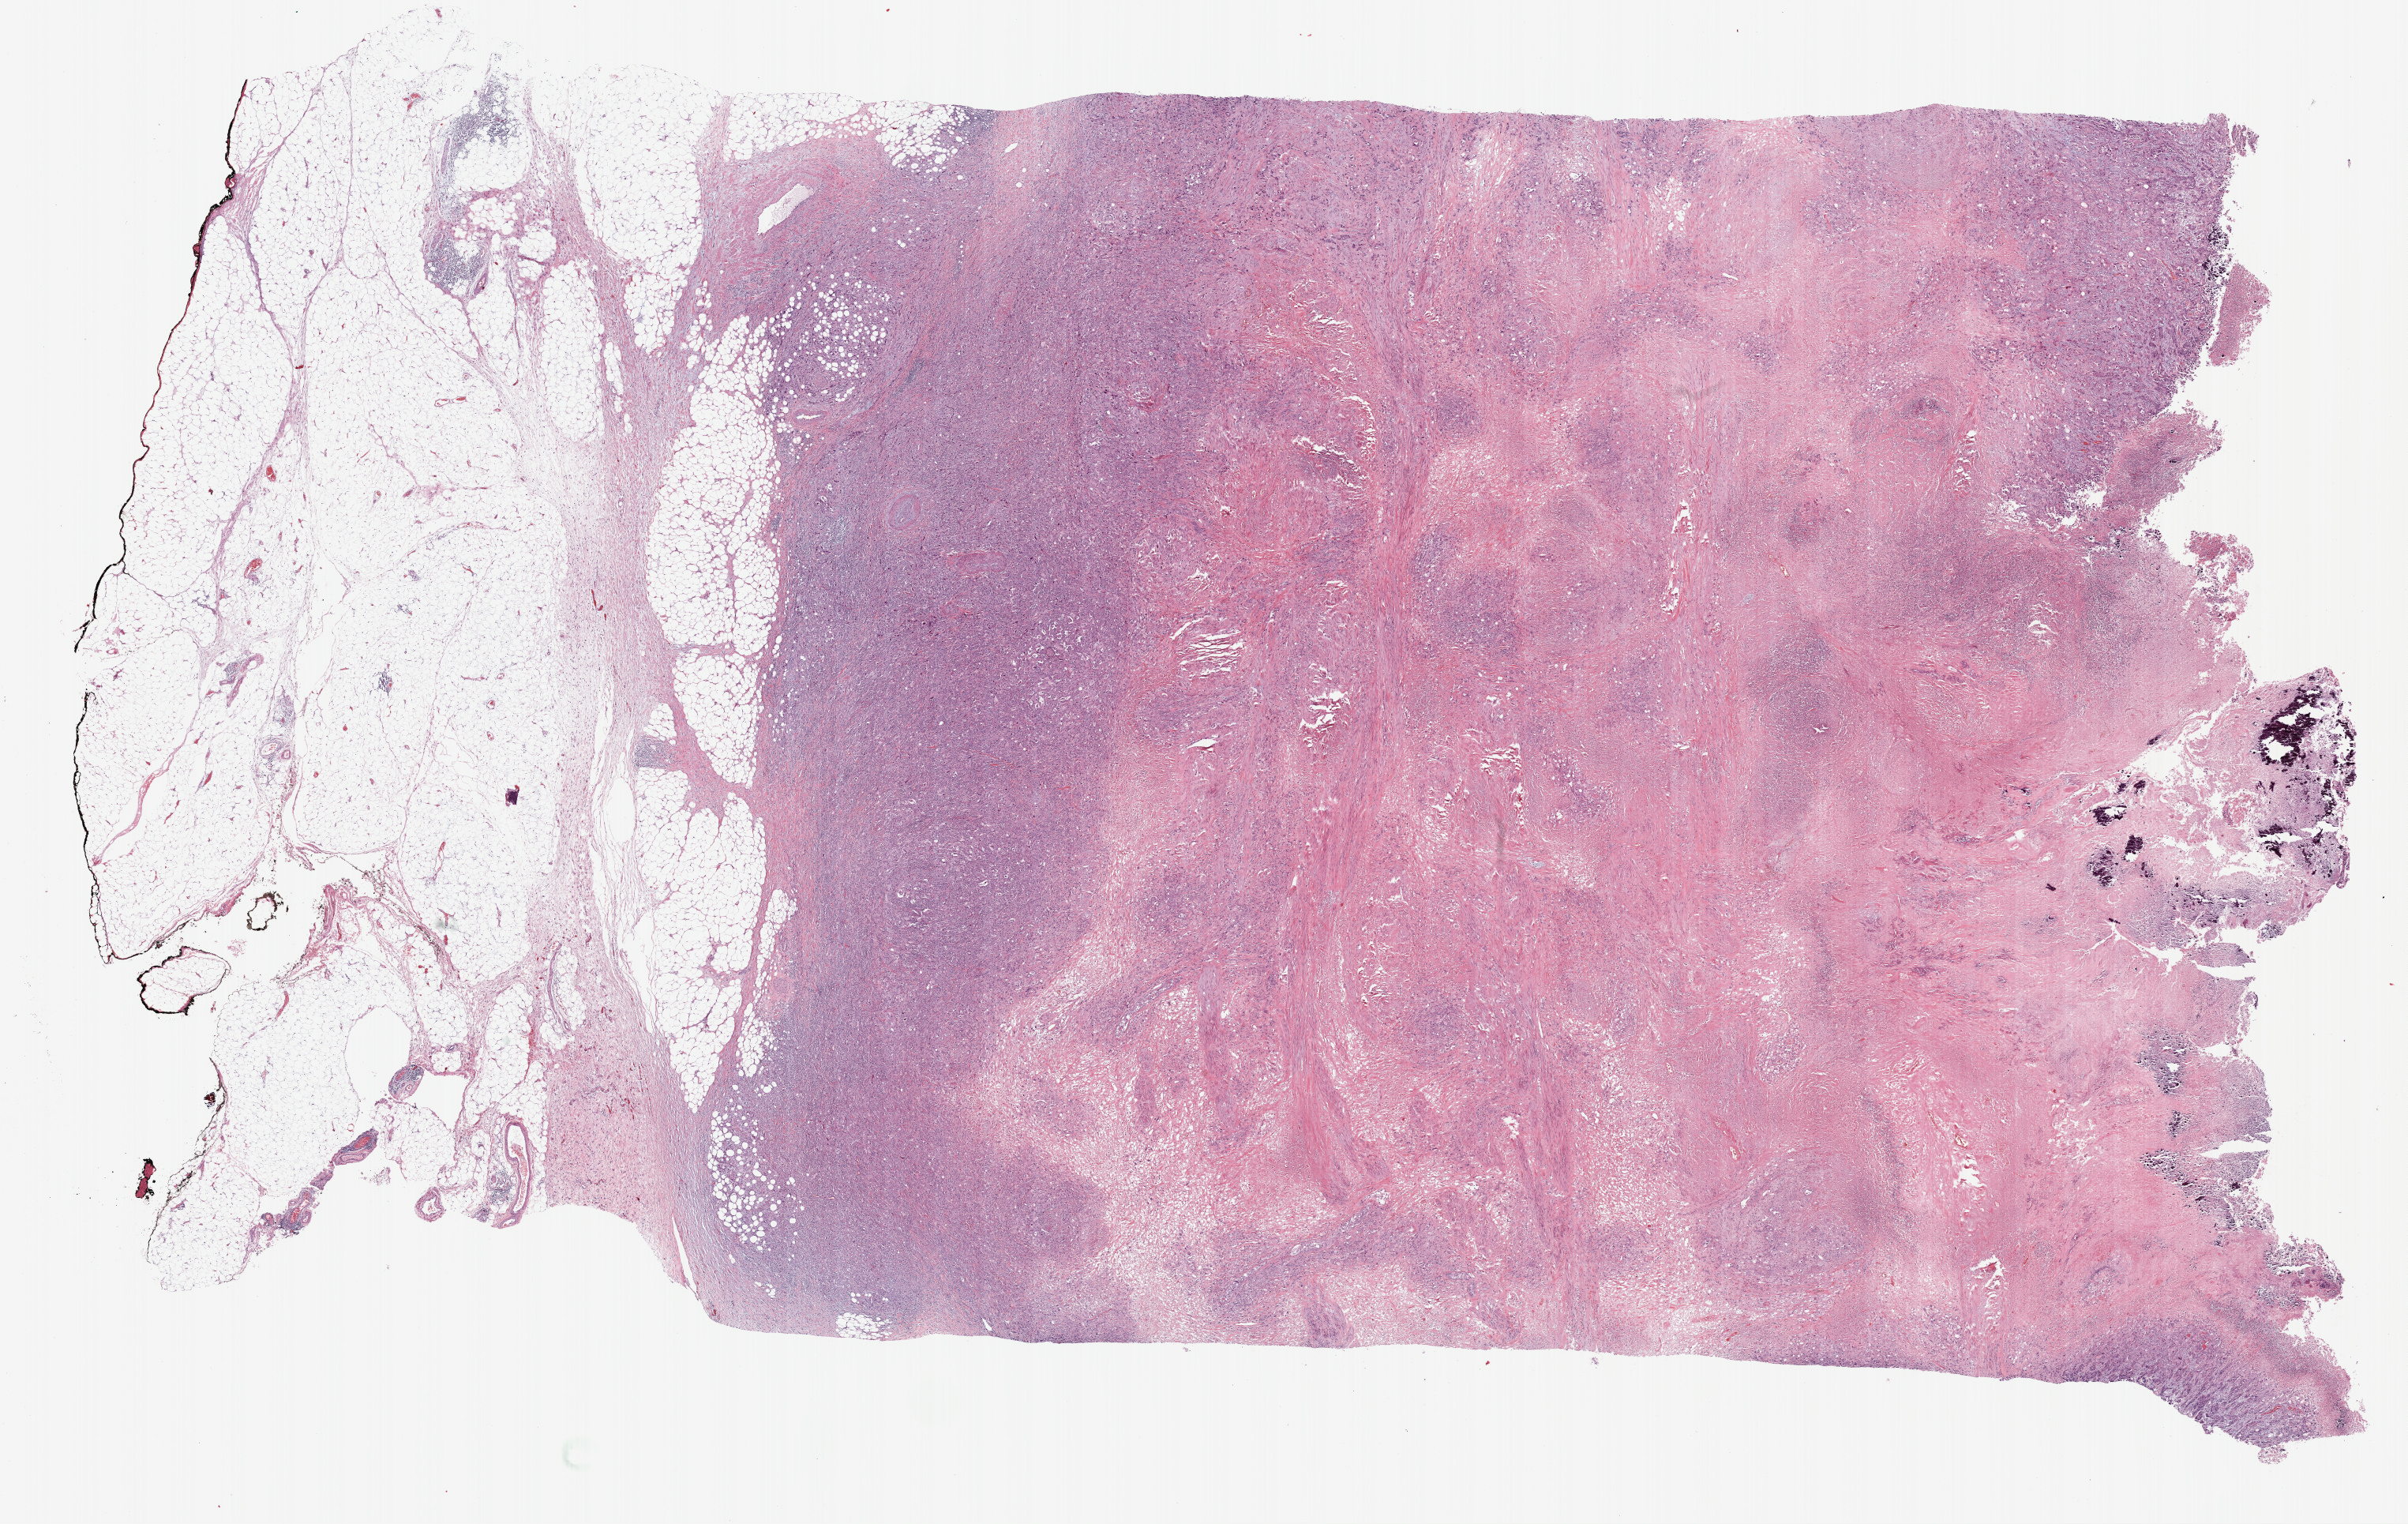
Digitized H&E tissue section (whole slide), whole scanned area (about 24.7 x 15.6 mm, slide scanned at 40x) shown as a low-resolution overview, formalin-fixed paraffin-embedded (FFPE) diagnostic section, bladder, primary tumour sample. Female, age 61 years at initial diagnosis. Histologic grade: high grade.
AJCC pathologic stage: III (6th edition). TNM: T3b N0 MX. Pathologic diagnosis: Transitional cell carcinoma.